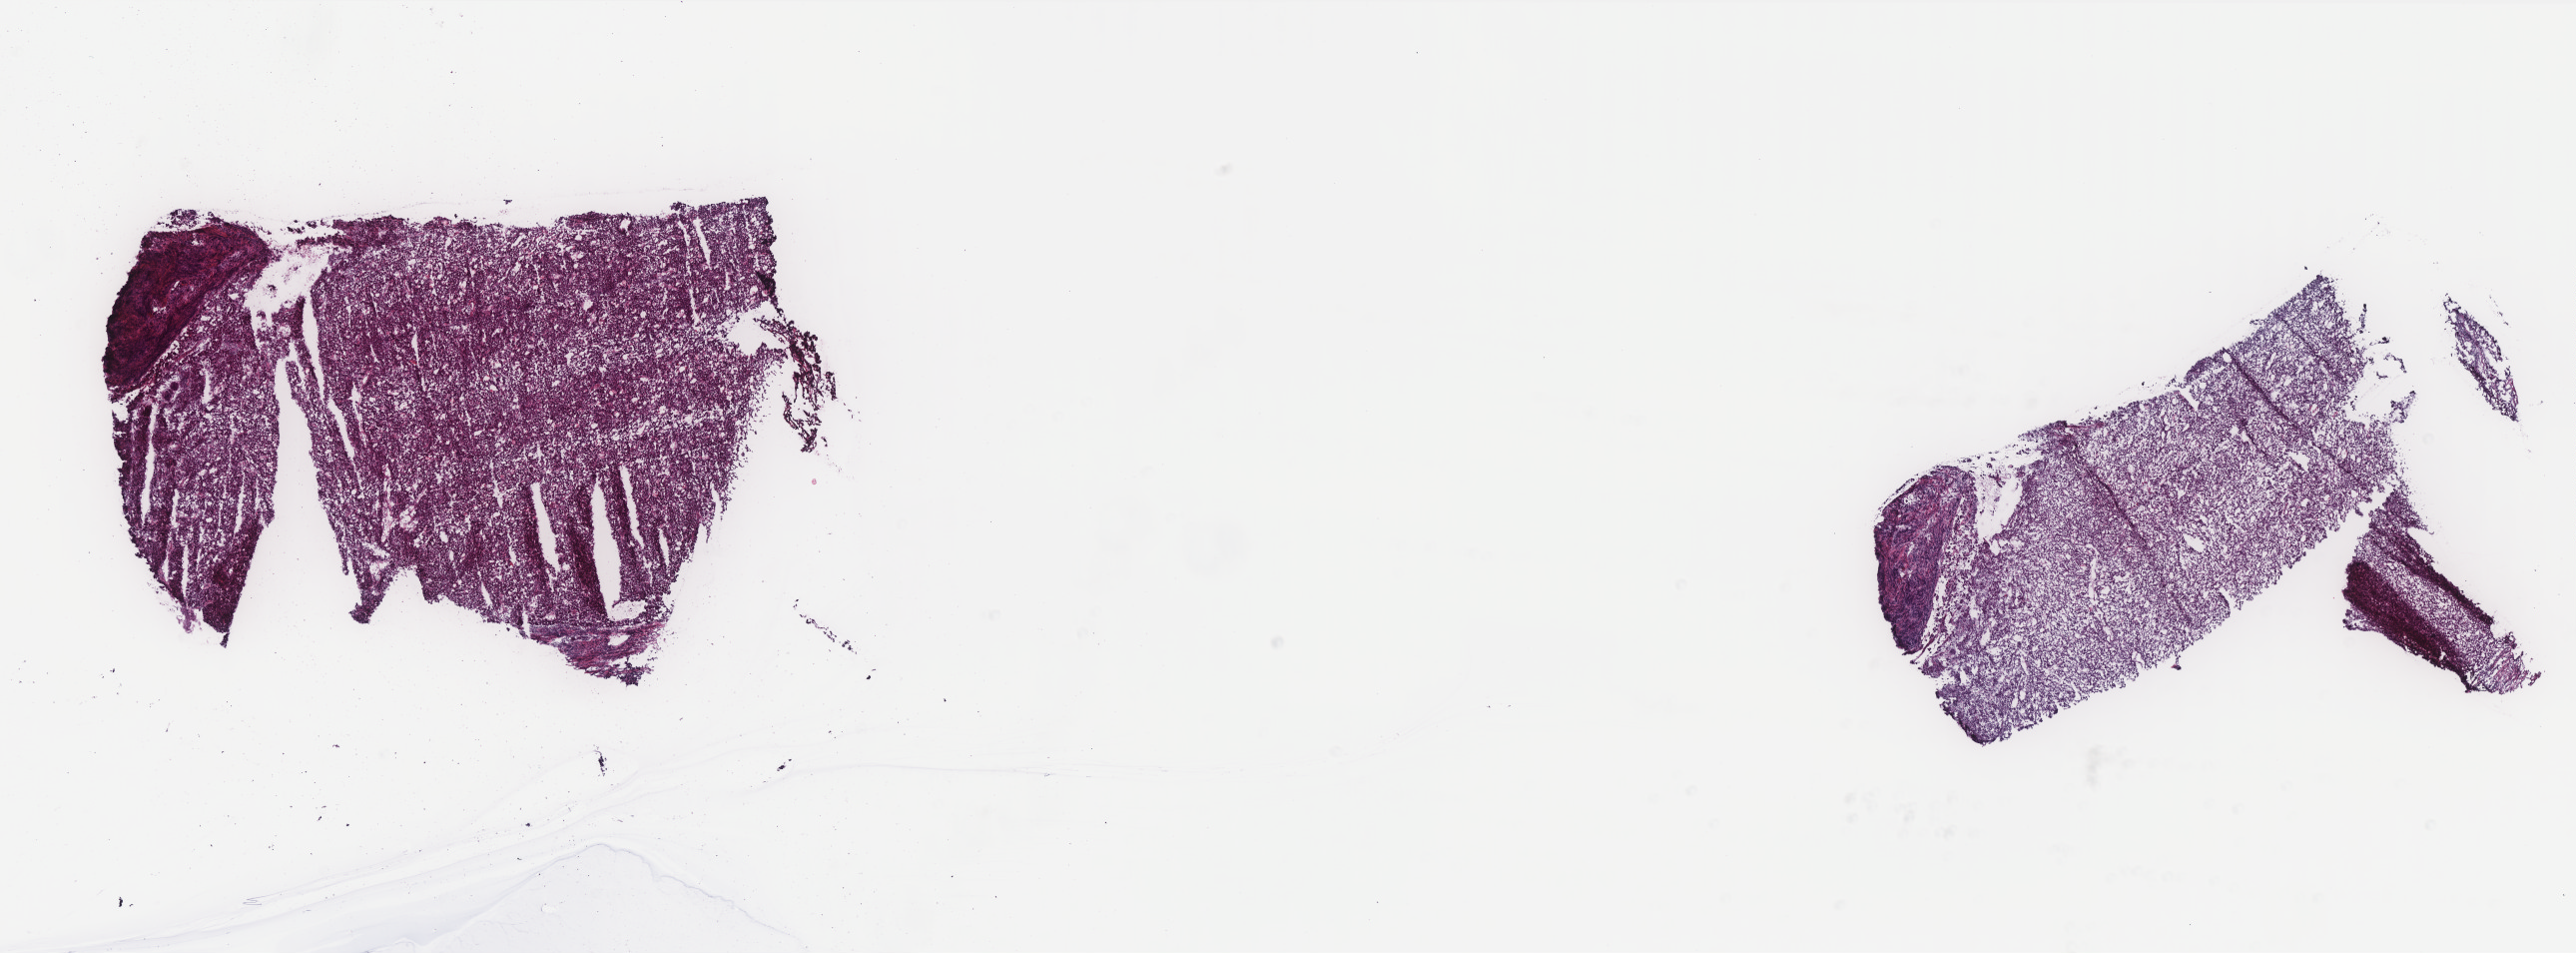
H&E whole-slide image — a low-resolution overview of the entire scanned area, about 20.7 x 7.6 mm (from a 40x scan), frozen section from the top of the tissue portion, sample: primary tumour, liver. Patient: female, age at initial diagnosis 20 years. Slide review estimates, as recorded: tumour cells 100%, tumour nuclei 95%.
Histologic diagnosis: Hepatocellular carcinoma, NOS.